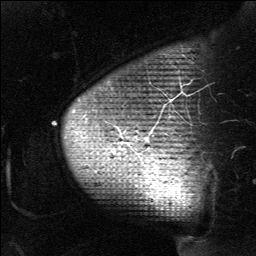
Breast MRI (dynamic contrast-enhanced), one sagittal slice; position 51 of 64 along the scan axis; dynamic contrast-enhanced study with each time point stored as its own series, time point 2 of 3 at this slice position (early post-contrast, ordered by acquisition time); 1.5 T; TE 4.8 ms, TR 27 ms; 2 mm slice thickness; 256 × 256 image matrix. Patient: female, 39 years. From the clinical record (not read from this slice): setting: breast cancer imaged before/during neoadjuvant chemotherapy; receptor status: HER2-positive.
Annotated regions visible in this slice (semi-automatic segmentation, software-assisted and operator-edited):
- analysis volume of interest (the breast-tissue region the enhancement analysis was run in; not a lesion): box from (x=62, y=44) to (x=201, y=216) px
- tumour enhancement mask (voxels above the 90 % enhancement threshold inside the analysis volume of interest): (x=146, y=193)–(x=150, y=194)